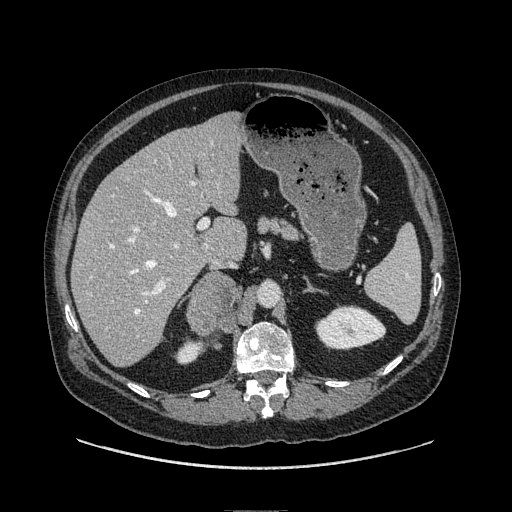
Contrast-enhanced abdominal CT, one axial slice. Slice 55 of 149 in the series (ordered by position). Soft-tissue window (W 400 / L 40 HU). 1.25 mm slice thickness. 512 × 512 image matrix, field of view 440 × 440 mm. Male patient. Case-level facts recorded for this patient, not image findings: diagnosis: adrenocortical carcinoma; tumour side: right adrenal; tumour size at pathology: 7.5 cm; Ki-67 index: 15 %.
Outlined on this slice (semi-automatically segmented with operator editing):
- mass: bounding box <187,275,238,332> (left, top, right, bottom; pixels)